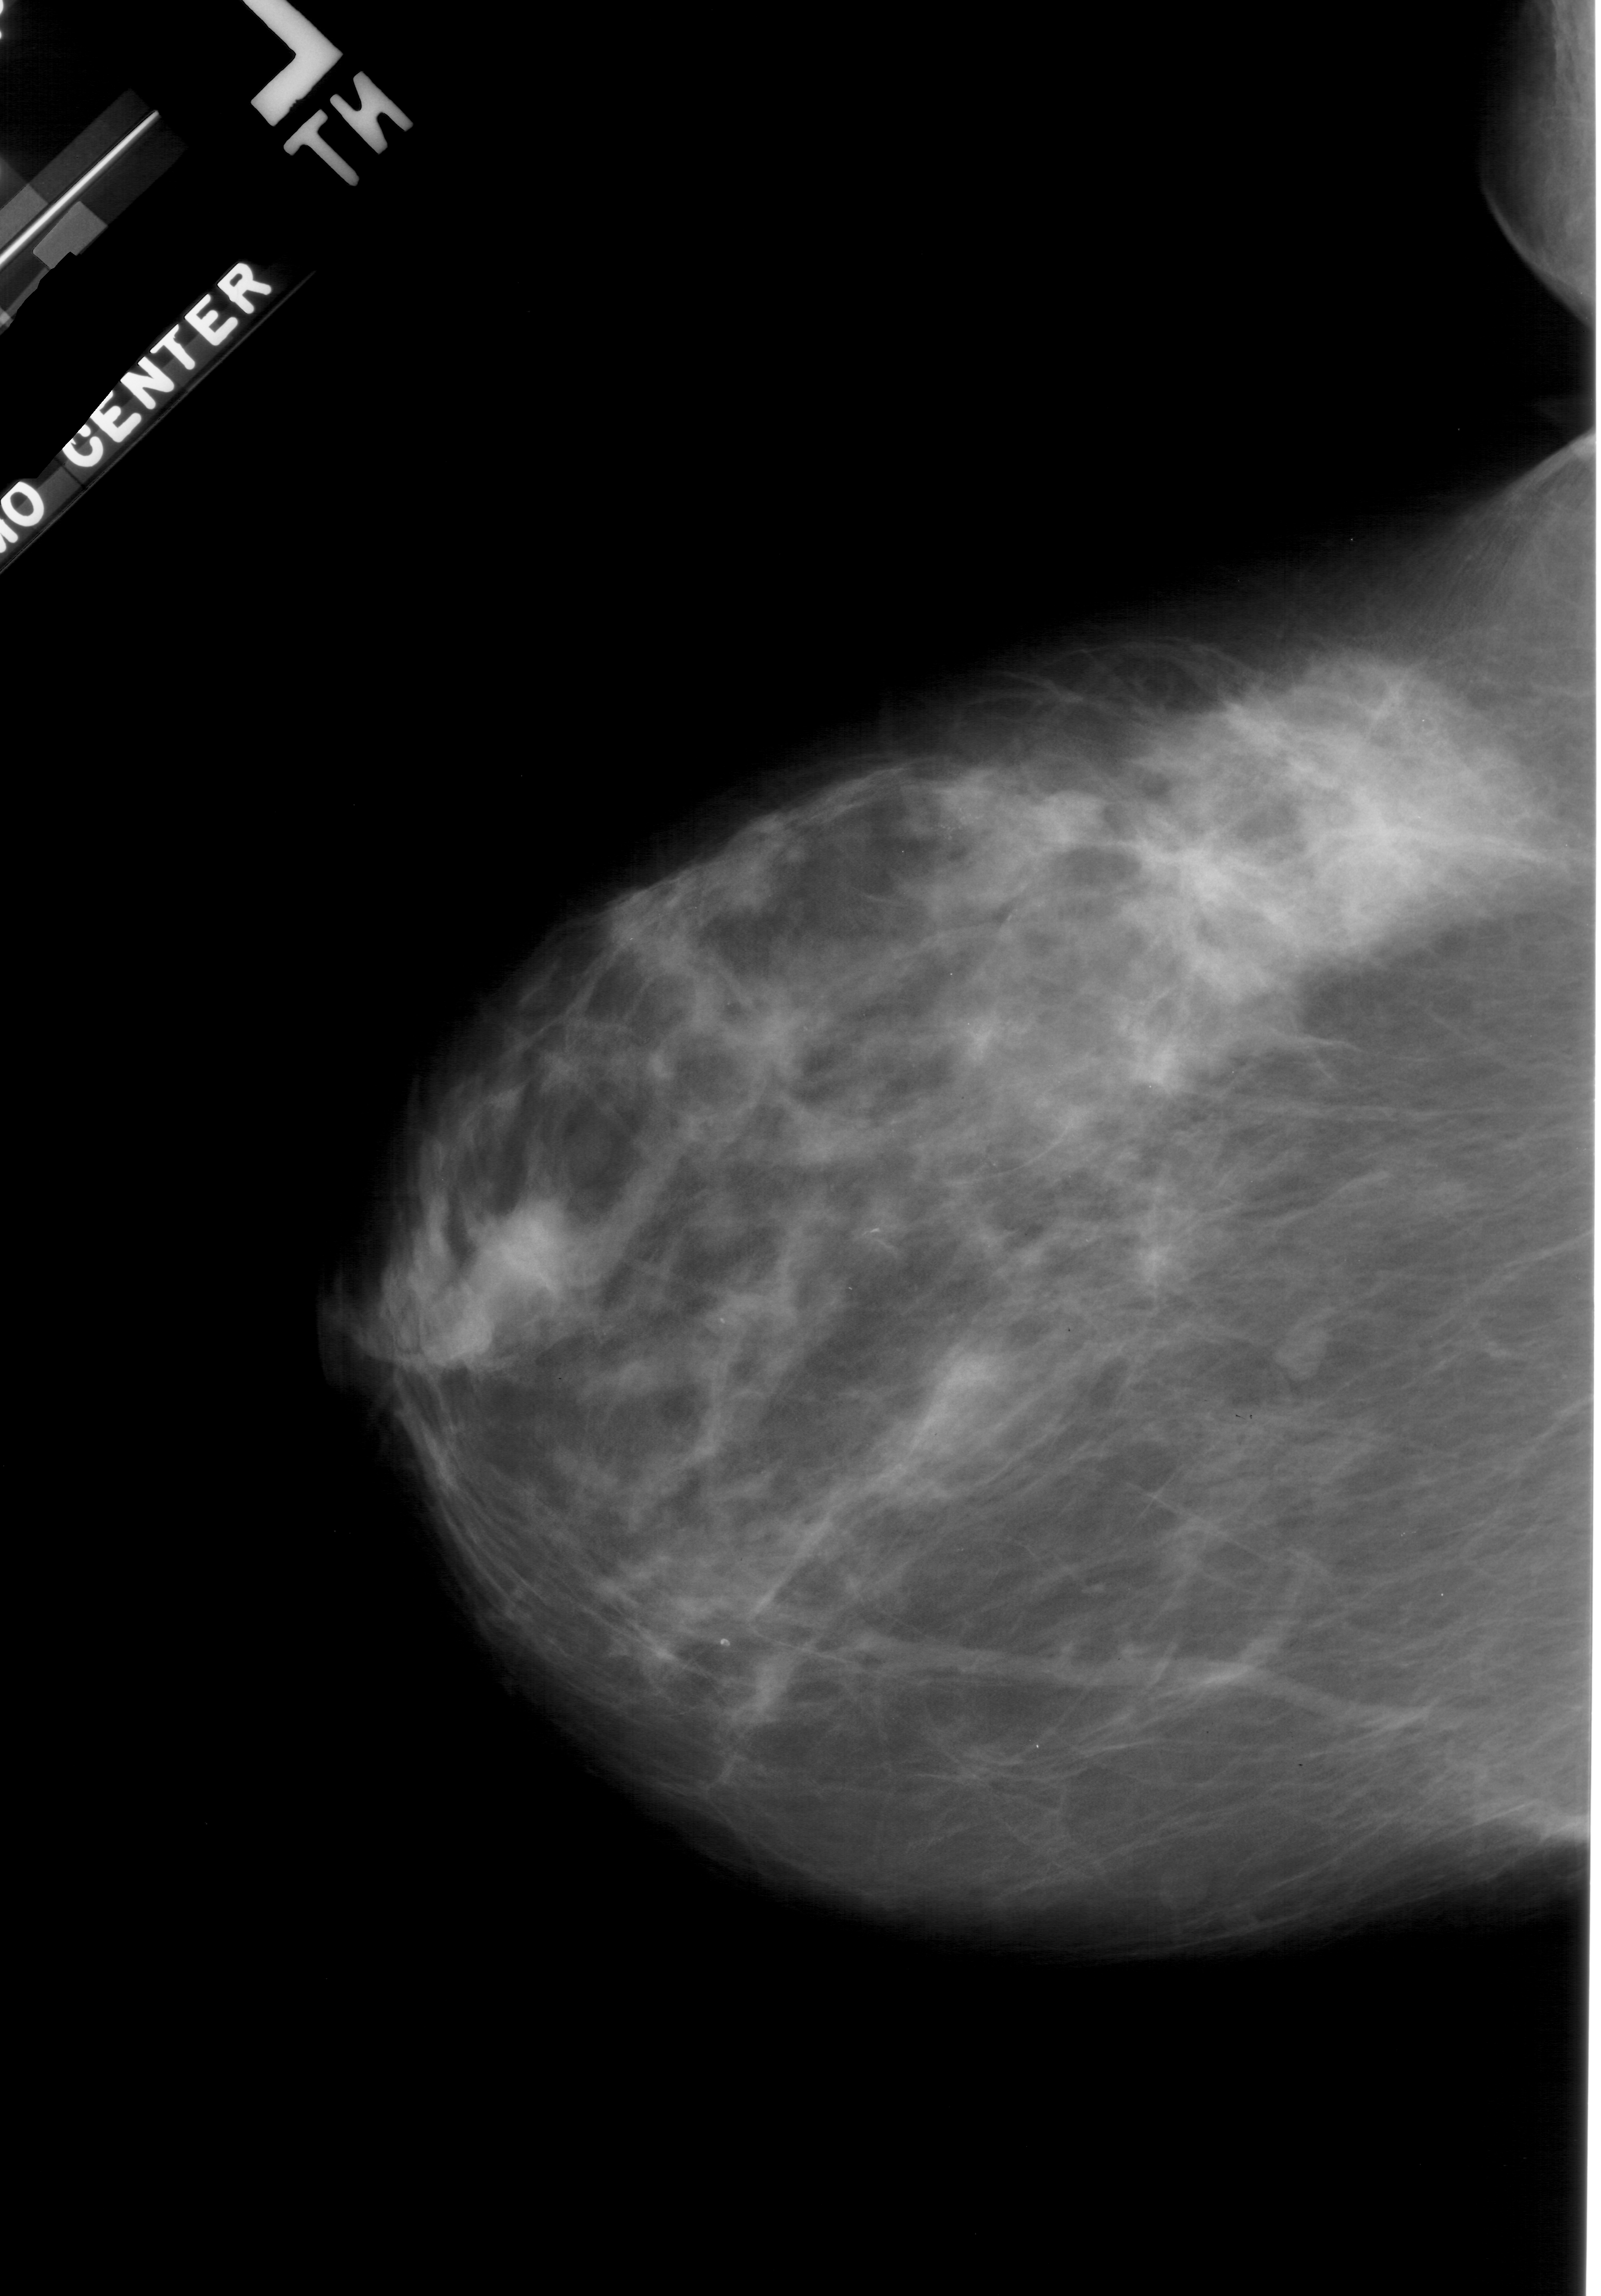
Digitized screen-film mammogram; left breast; CC view; breast composition: heterogeneously dense (BI-RADS density category 3 of 4).
- Finding: calcifications, morphology pleomorphic, distribution clustered; BI-RADS assessment category 4; subtlety rating 2 on a 1 (subtle) to 5 (obvious) scale; pathology result (as recorded, not read from the image): benign.